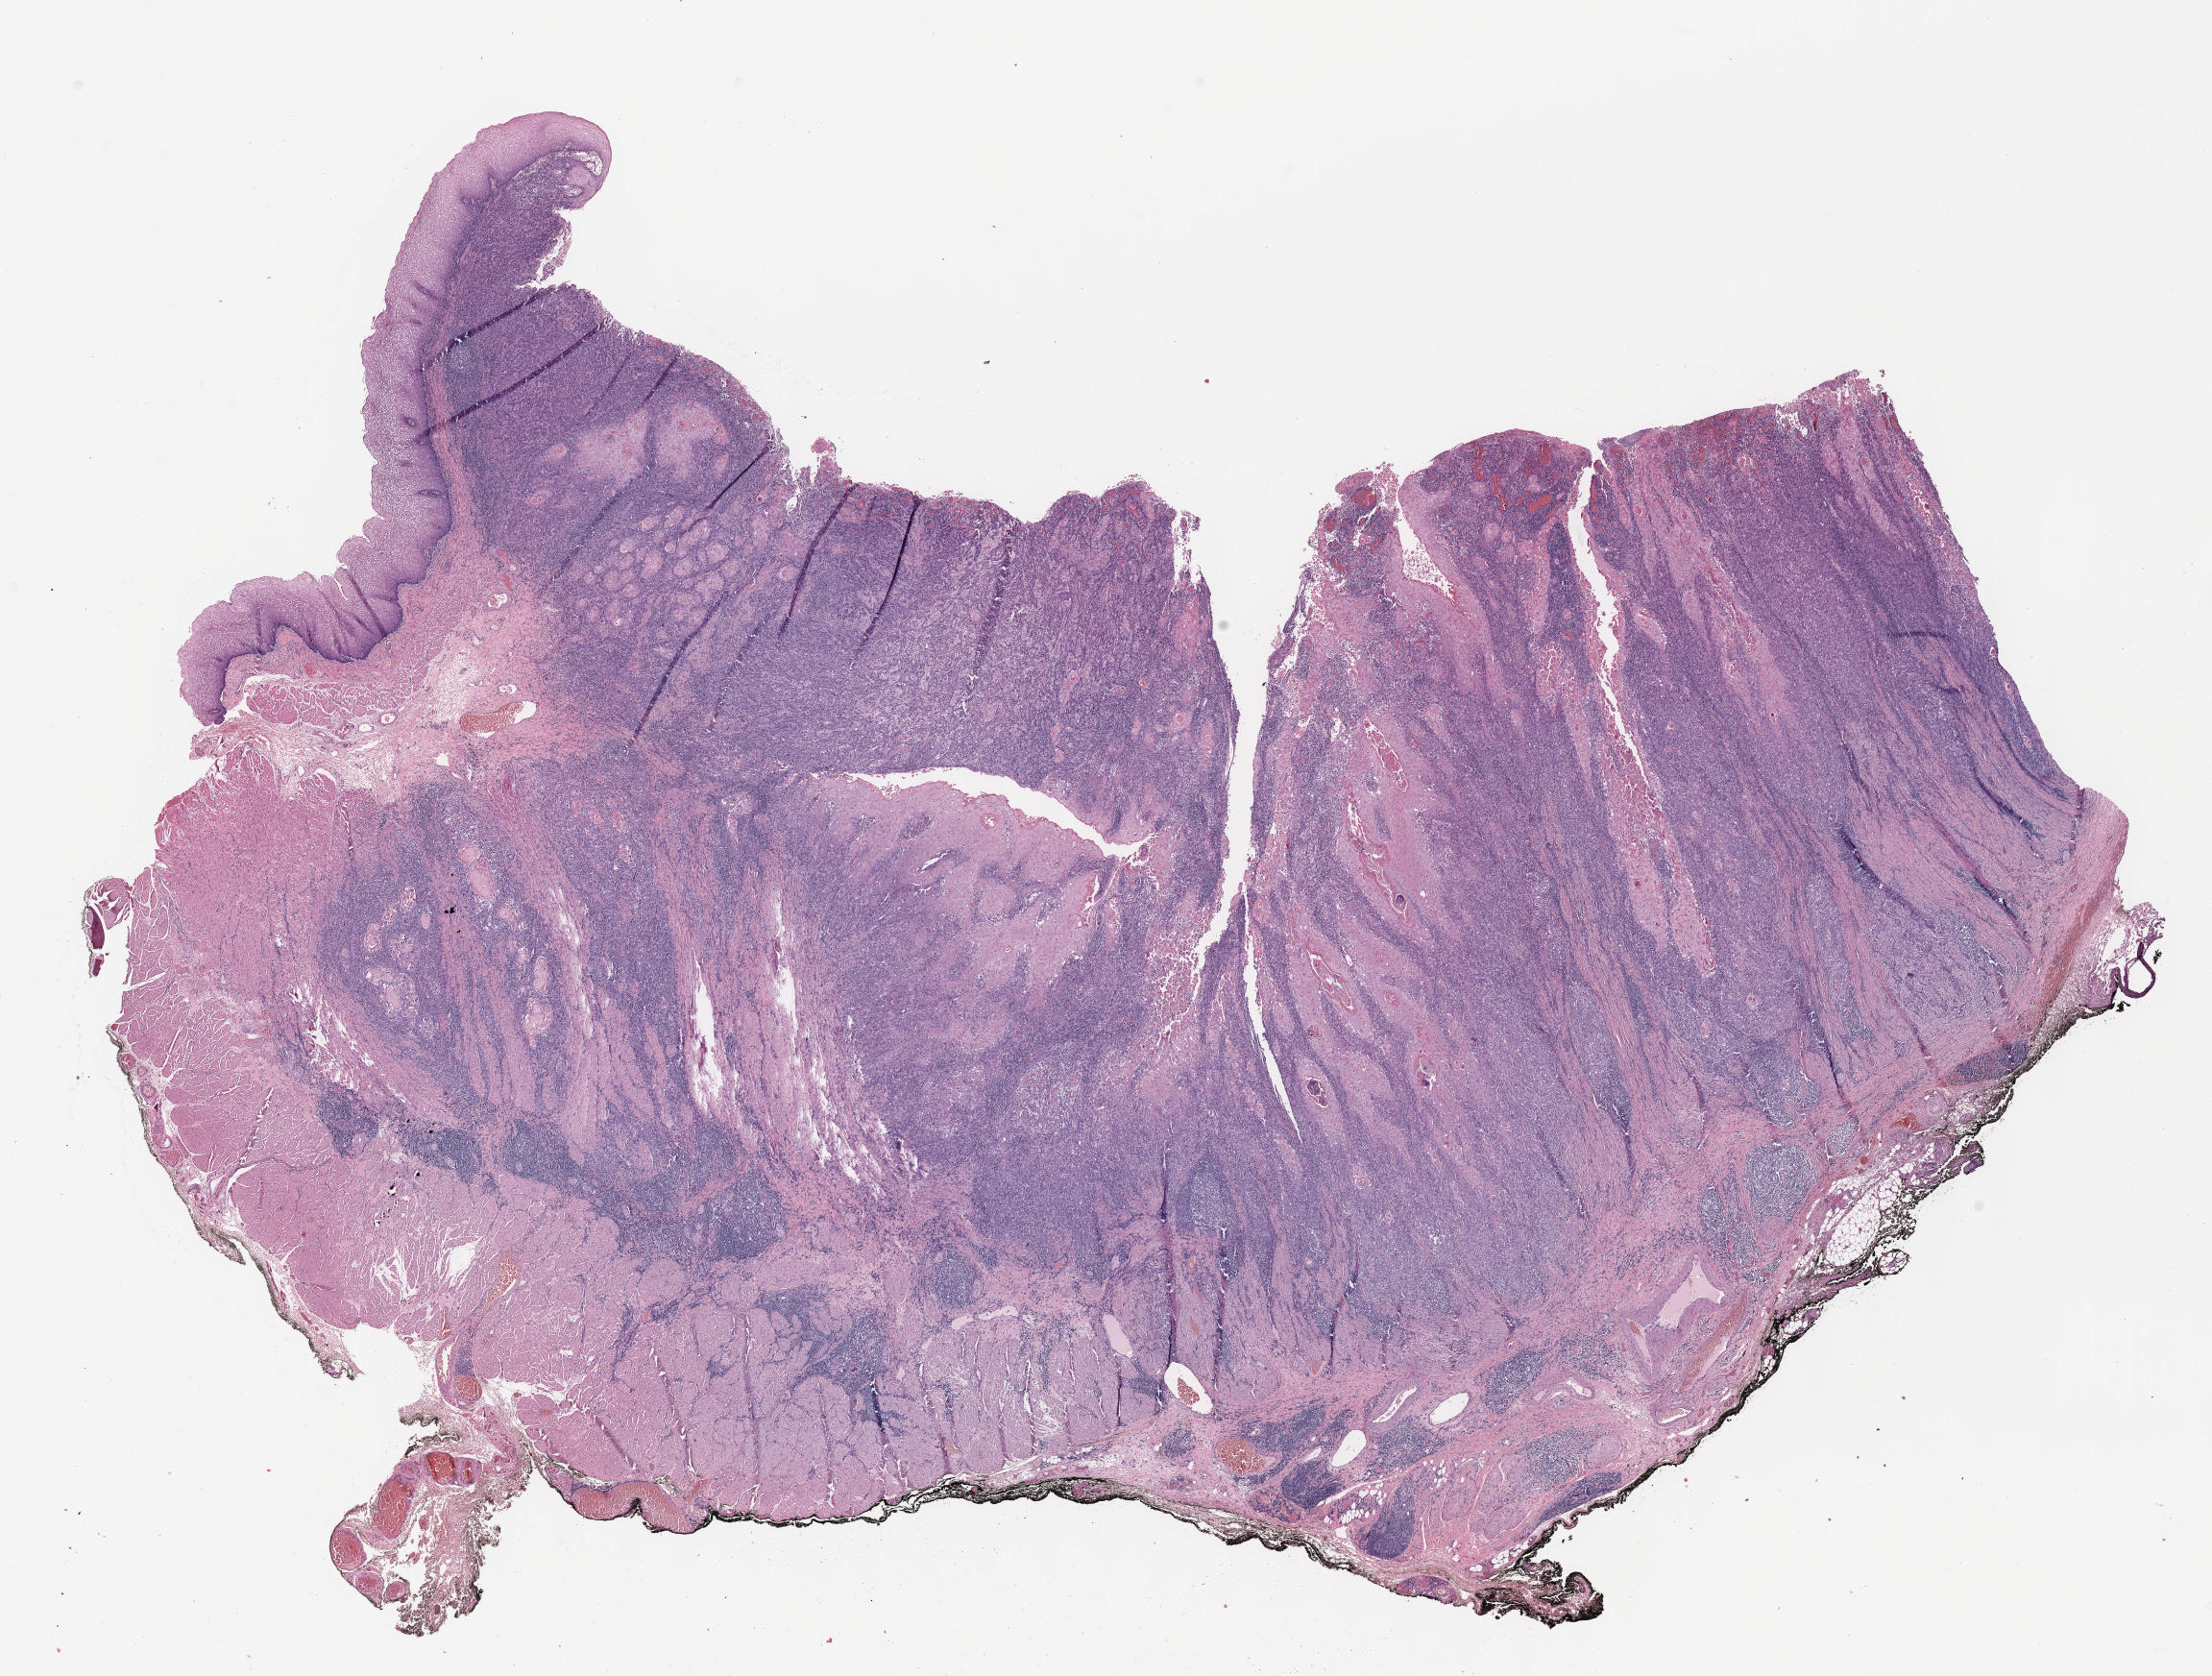
Digitized H&E-stained tissue section (whole slide) — low-resolution overview of the scanned area, about 18.6 x 14.1 mm (acquisition: 40x scan), FFPE section, primary tumour sample from the esophagus. Patient: male, age at initial diagnosis 58 years.
Diagnosis: Squamous cell carcinoma, NOS.